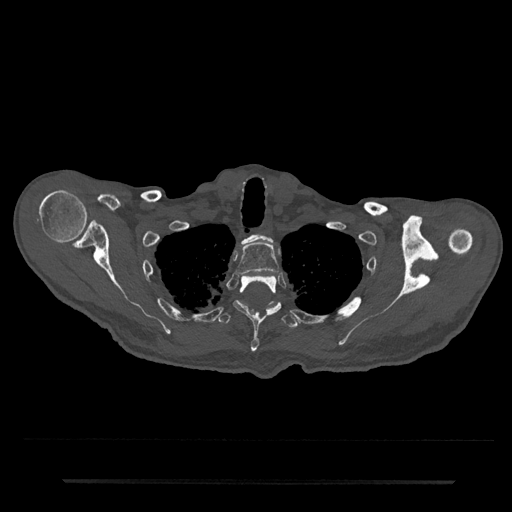
CT including the spine, one axial slice. Position 661 of 797 along the scan axis. Reconstruction kernel Br40s/3. 120 kVp. Bone window (W 1800 / L 400 HU). 0.5 mm slice thickness. 512 × 512 image matrix. Male patient, age 74 years. From the clinical record (not read from this slice): primary cancer: prostate.
Outlined on this slice (semi-automatically segmented with operator editing):
- T1 vertebra: bounding box [x1, y1, x2, y2] px = [242, 234, 274, 243]
- T2 vertebra: [236, 242, 279, 277]
- T3 vertebra: [233, 275, 282, 353]
- T4 vertebra: [217, 301, 298, 329]